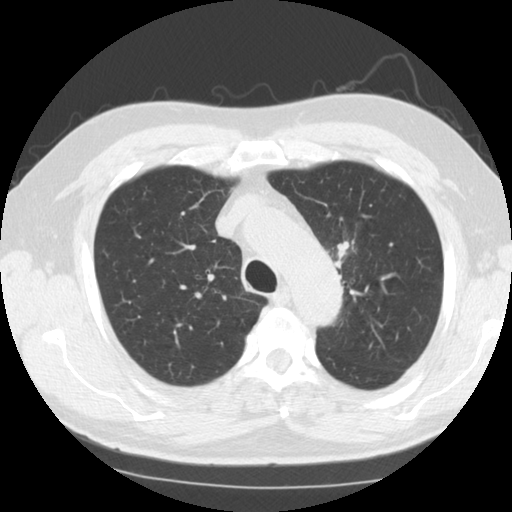
Low-dose screening chest CT, one axial slice. Slice 96 of 124 in the series (ordered by position). Reconstruction kernel STANDARD. 120 kVp. Lung window (W 1500 / L -600 HU). 2.5 mm slice thickness. 512 × 512 image matrix.
Structures marked on this image (manually delineated by an expert):
- lesion 1 (tumor, upper lobe of left lung): bounding box <337,242,349,260> (left, top, right, bottom; pixels)